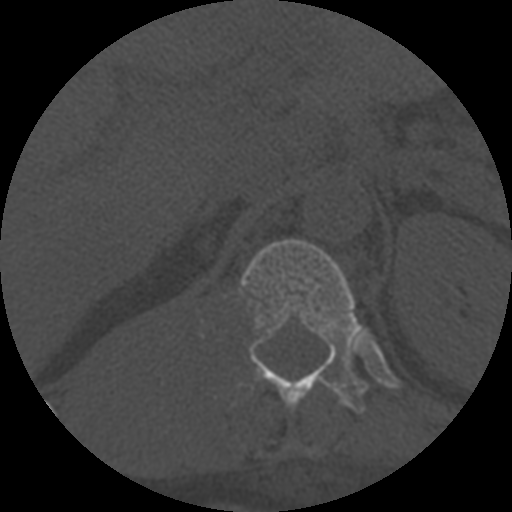
CT including the spine, one axial slice; slice 315 of 708 in the series (ordered by position); 120 kVp; one of 3 acquisitions stored at this slice position; bone window (W 1800 / L 400 HU); 1.25 mm slice thickness; 512 × 512 image matrix, field of view 160 × 160 mm. Patient age 55 years. From the clinical record (not read from this slice): primary cancer: colon.
Outlined on this slice (semi-automatically segmented with operator editing):
- T12 vertebra: box from (x=239, y=239) to (x=367, y=413) px